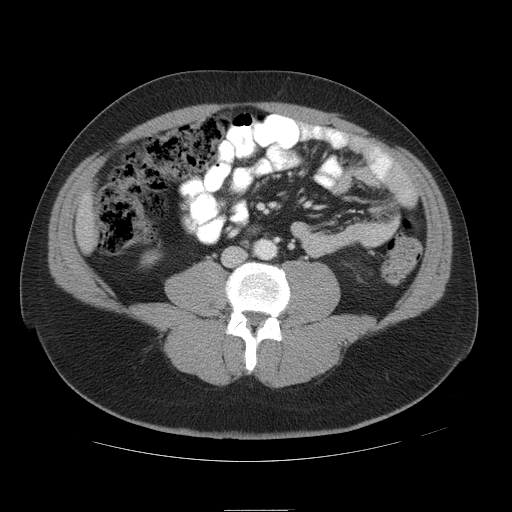
Contrast-enhanced abdominal CT, one axial slice. Slice 9 of 49 in the series (ordered by position). Reconstruction kernel STANDARD. Soft-tissue window (W 400 / L 40 HU). 512 × 512 image matrix, field of view 425 × 425 mm. Male patient, age 52 years. Case-level facts recorded for this patient, not image findings: diagnosis: colorectal cancer liver metastases, imaged before liver resection; multiple liver metastases: yes; largest metastasis: 5.1 cm; disease in both lobes: yes.
Outlined on this slice (manually delineated by an expert):
- liver: bounding box (x1, y1, x2, y2) in pixels: (77, 200, 94, 247)